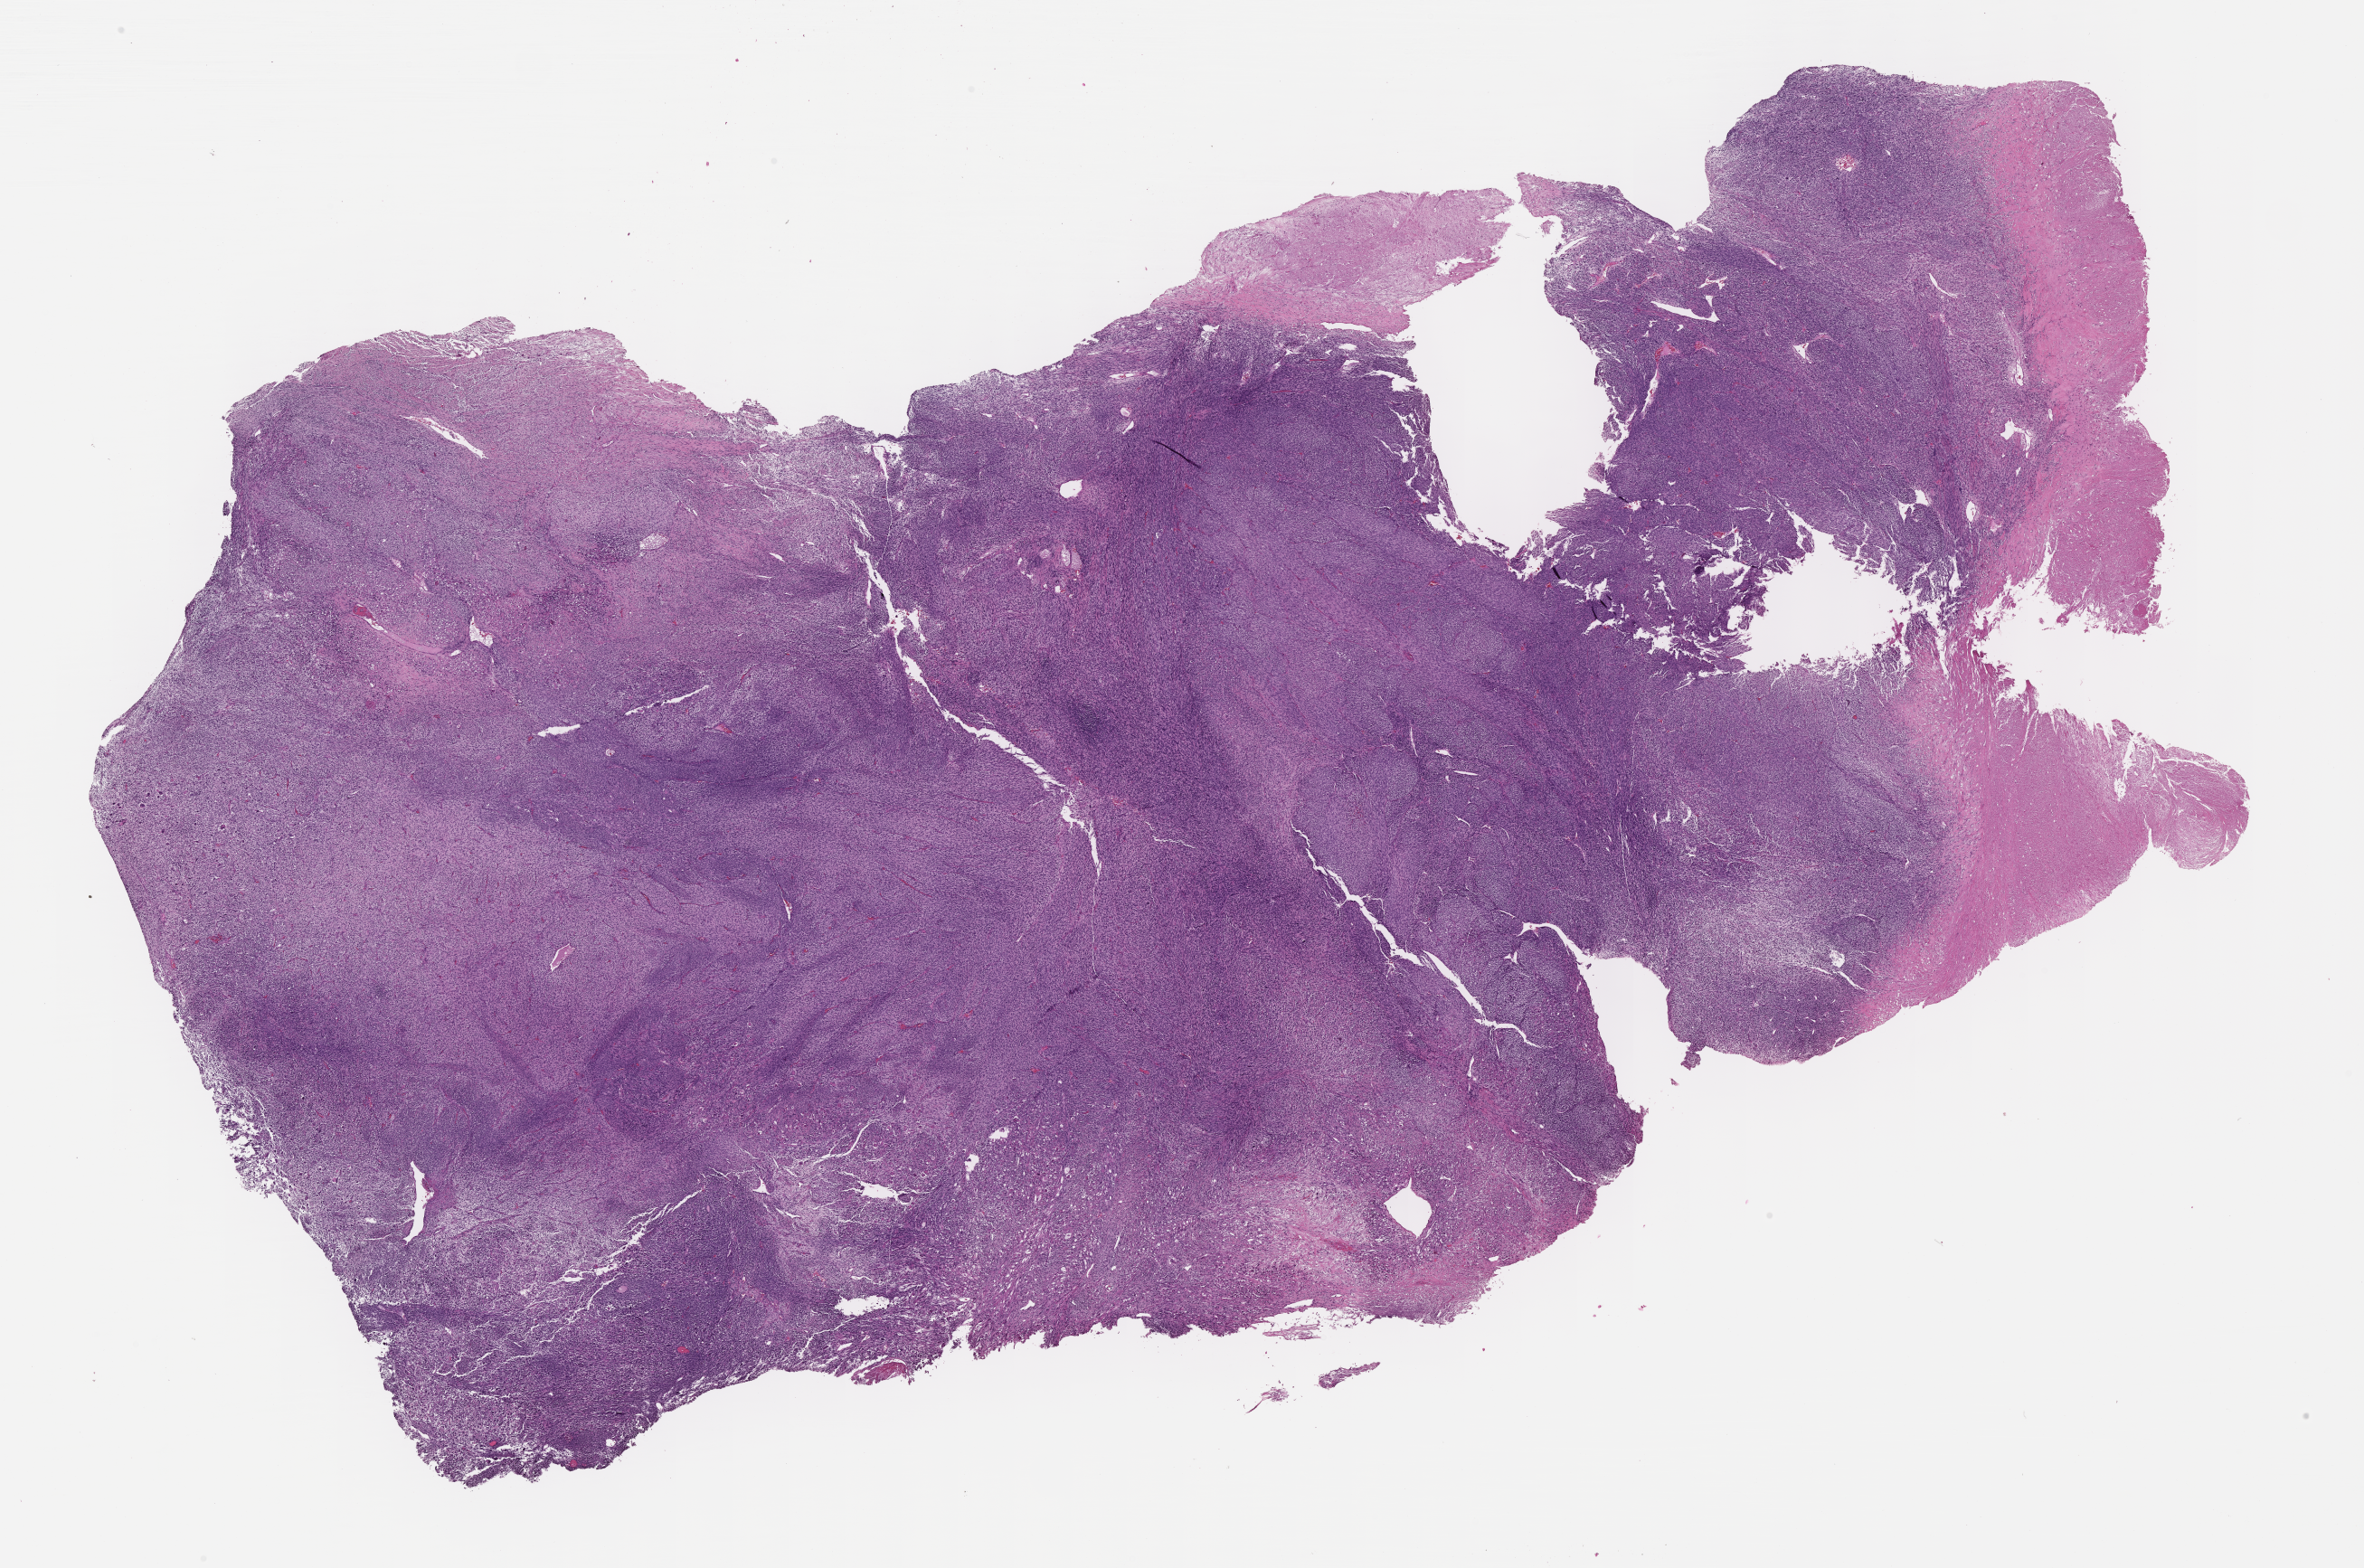
H&E whole-slide image of tumor tissue — shown as a low-resolution overview of the whole scanned area (about 21.1 x 14.0 mm), FFPE section, site: testicle, left. Patient: male, age 13.5 years at diagnosis.
Diagnosis: rhabdomyosarcoma; histological classification: embryonal rhabdomyosarcoma.